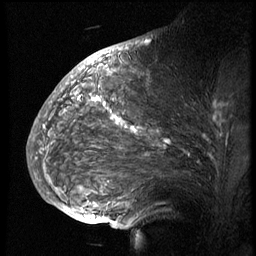
Breast MRI (dynamic contrast-enhanced), one sagittal slice; position 39 of 74 along the scan axis; 3 images stored at this slice position (order not interpretable as contrast timing); 1.5 T; TE 4.2 ms, TR 8.9 ms; 2.5 mm slice thickness; 256 × 256 image matrix. Patient: female, 57 years. Case-level facts recorded for this patient, not image findings: setting: breast cancer imaged before/during neoadjuvant chemotherapy; receptor status: HER2-positive.
Structures marked on this image (semi-automatically segmented with operator editing):
- analysis volume of interest (the breast-tissue region the enhancement analysis was run in; not a lesion): box from (x=51, y=67) to (x=249, y=173) px
- tumour enhancement mask (voxels above the 140 % enhancement threshold inside the analysis volume of interest): (x=92, y=97)–(x=168, y=142)